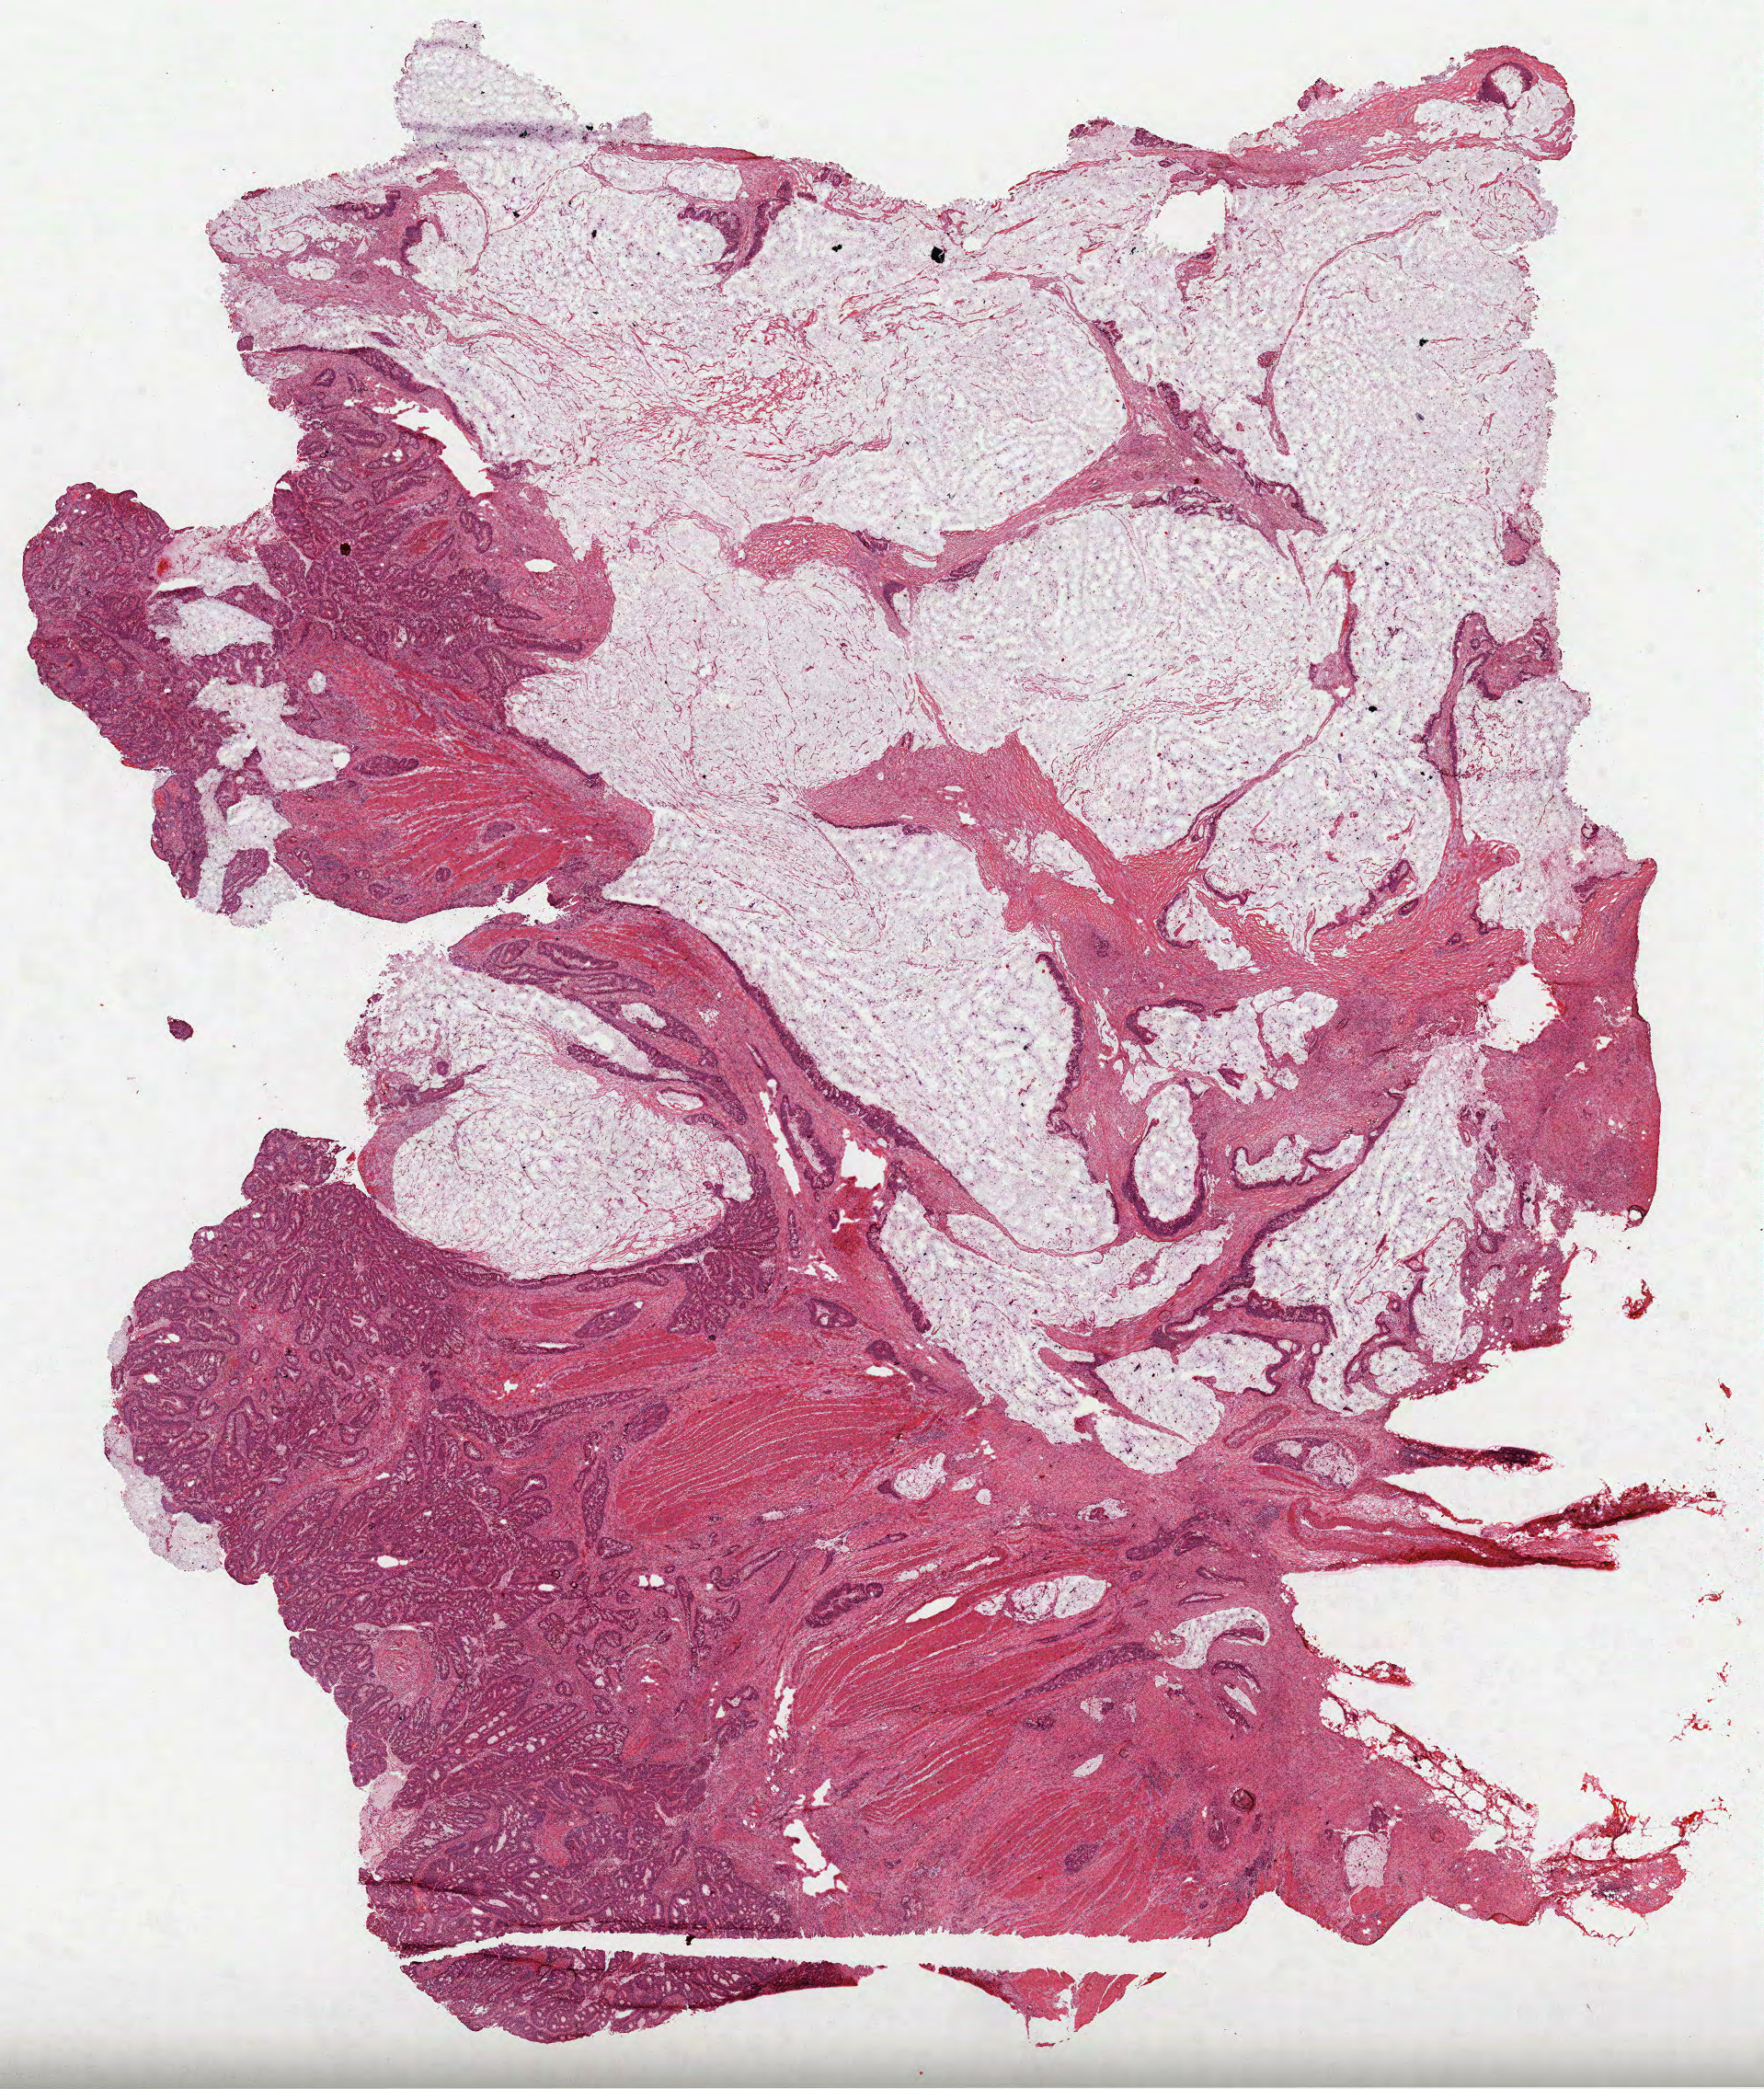
Whole-slide histology image, H&E-stained — a low-resolution overview of the entire scanned area, about 15.5 x 18.3 mm (from a 40x scan). Formalin-fixed paraffin-embedded (FFPE) diagnostic section. Sample: primary tumour, colon. Patient: male, age at initial diagnosis 53 years.
AJCC pathologic stage: IIIB. Lymph nodes positive (case pathology): 1 of 23 examined. Diagnosis: Mucinous adenocarcinoma (transverse colon).